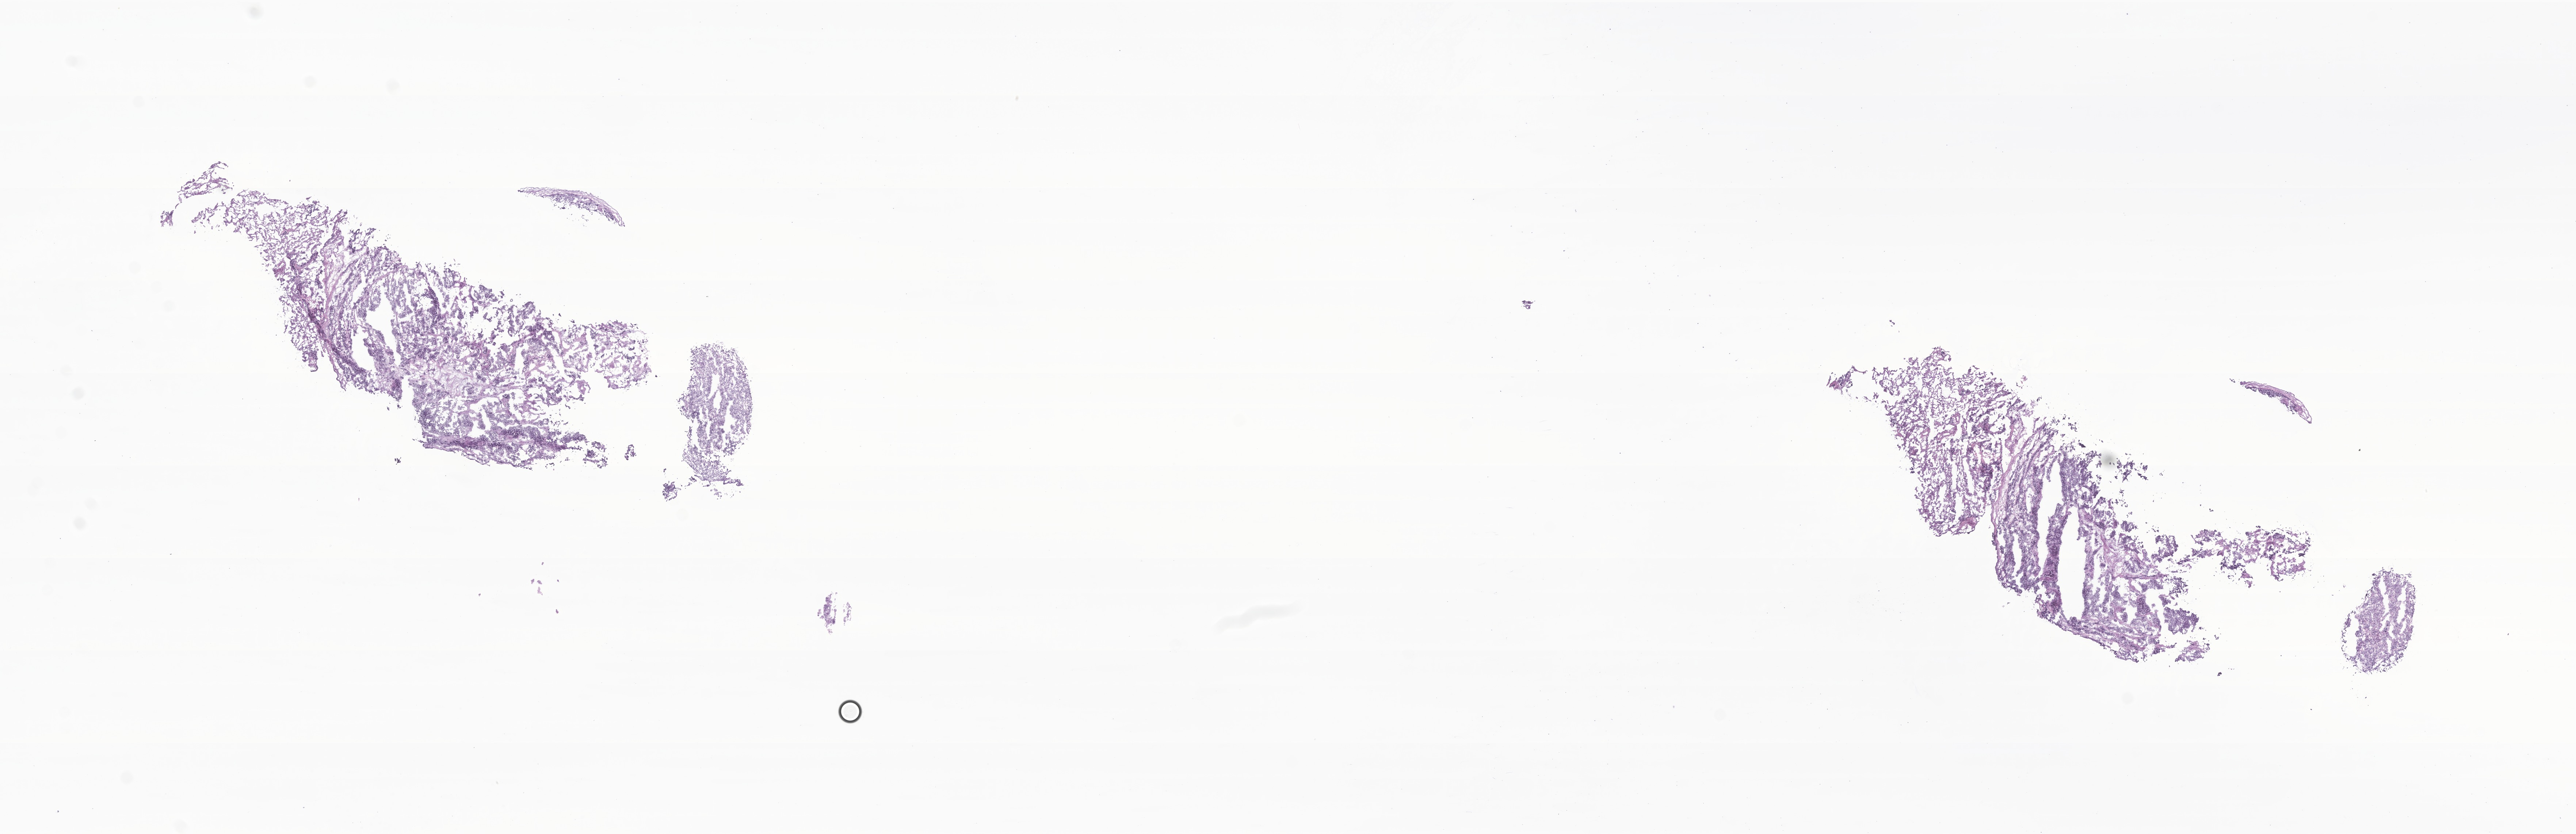
Digitized H&E-stained section of tumor tissue from the thorax — whole scanned area (about 29.7 x 9.6 mm) shown as a low-resolution overview, cryosection (OCT / tissue freezing medium). Patient: male, age 177 months (14 years 9 months).
• diagnosis (ICD-O-3 morphology term): Small cell carcinoma, NOS